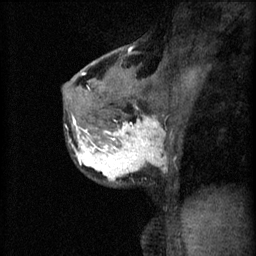
Breast MRI (dynamic contrast-enhanced), one sagittal slice; slice 37 of 60 in the series (ordered by position); 3 images stored at this slice position (order not interpretable as contrast timing); 1.5 T; TE 4.2 ms, TR 11 ms; 2 mm slice thickness; 256 × 256 image matrix. Female patient, age 37 years.
Structures marked on this image (semi-automatic segmentation, software-assisted and operator-edited):
- analysis volume of interest (the breast-tissue region the enhancement analysis was run in; not a lesion): bounding box (x1, y1, x2, y2) in pixels: (68, 118, 169, 187)
- tumour enhancement mask (voxels above the 70 % enhancement threshold inside the analysis volume of interest): (69, 118, 166, 181)